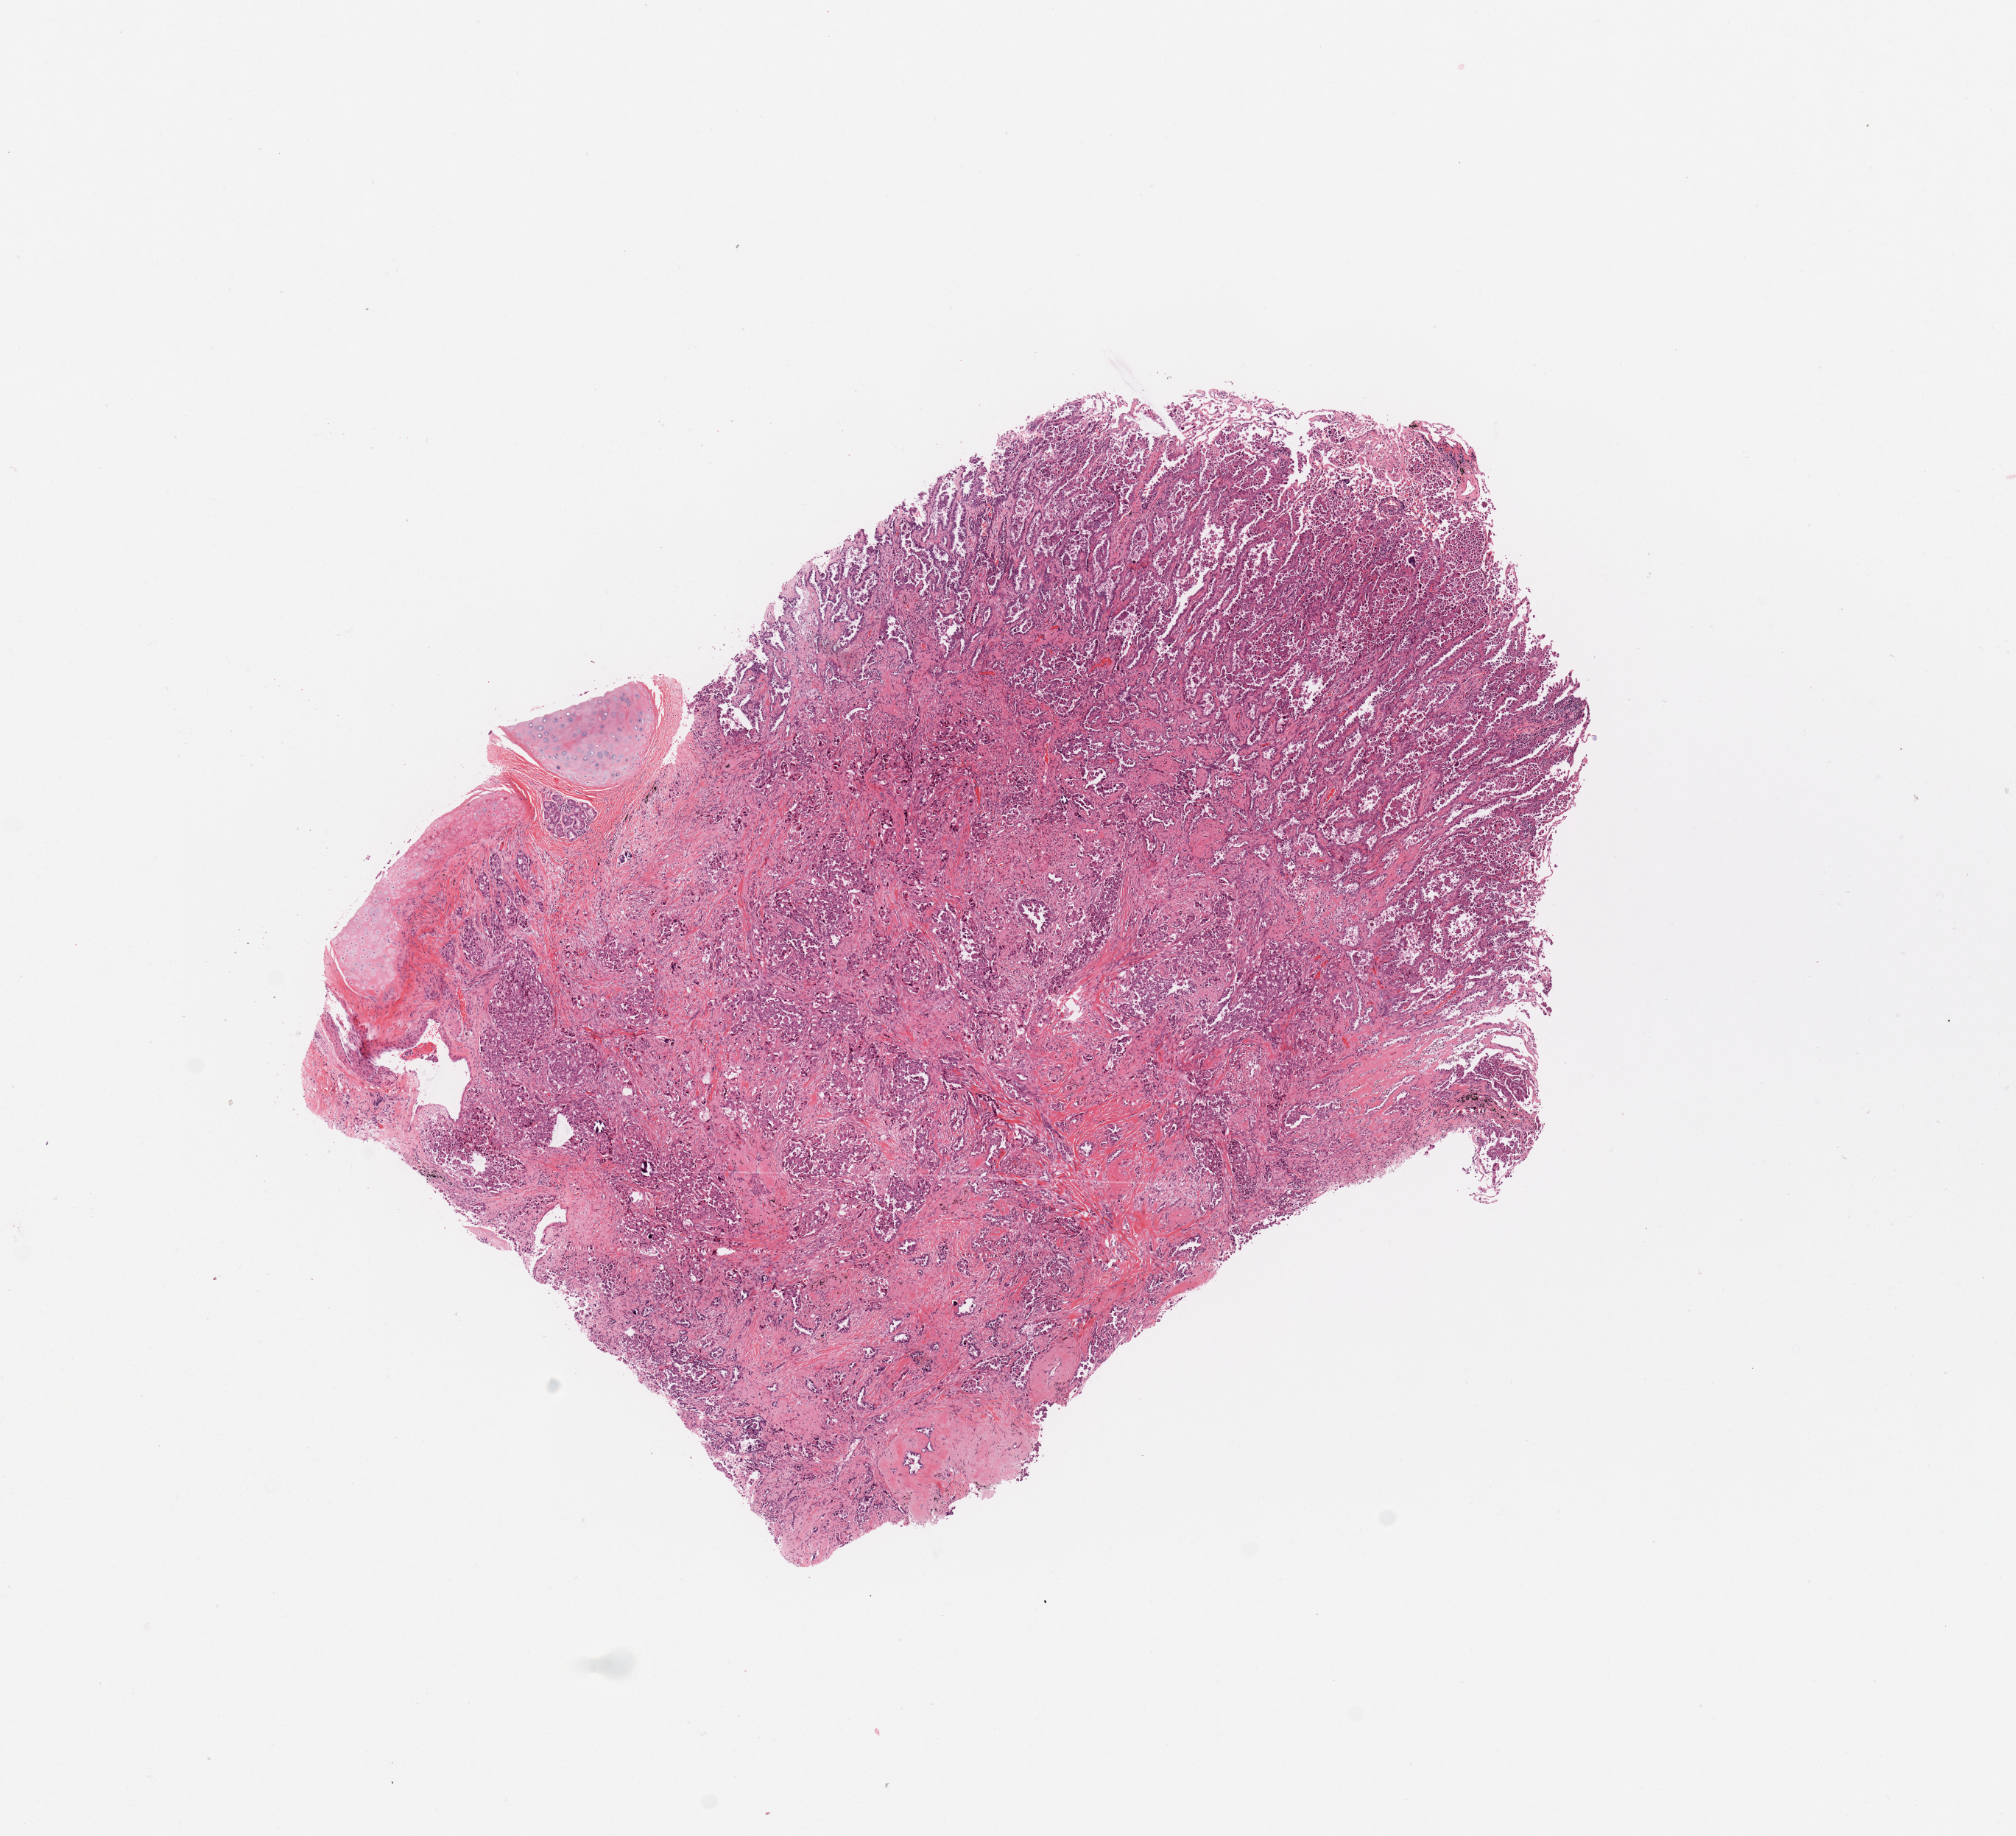
Whole-slide histology image, H&E, a low-resolution overview of the entire scanned area, about 10.8 x 9.9 mm (from a 20x scan), tumour tissue sample, sampled site: lung. Male, 58 y/o. Histologic grade: G3 (poorly differentiated). Pathologist review of this section (percent, as recorded): tumour nuclei 70%, necrosis 2%.
Primary tumour site (as recorded): right lower lobe. AJCC pathologic stage: IA. Diagnosis: Adenocarcinoma, NOS.